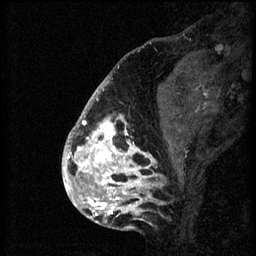
Breast MRI (dynamic contrast-enhanced), one sagittal slice. Slice 20 of 60 in the series (ordered by position). 3 images stored at this slice position (order not interpretable as contrast timing). 1.5 T. TE 4.2 ms, TR 8.2 ms. 2 mm slice thickness. 256 × 256 image matrix, field of view 180 × 180 mm. Patient: female, 41 years.
Outlined on this slice (semi-automatic segmentation, software-assisted and operator-edited):
- analysis volume of interest (the breast-tissue region the enhancement analysis was run in; not a lesion): box from (x=72, y=108) to (x=176, y=205) px
- tumour enhancement mask (voxels above the 70 % enhancement threshold inside the analysis volume of interest): (x=72, y=108)–(x=164, y=205)